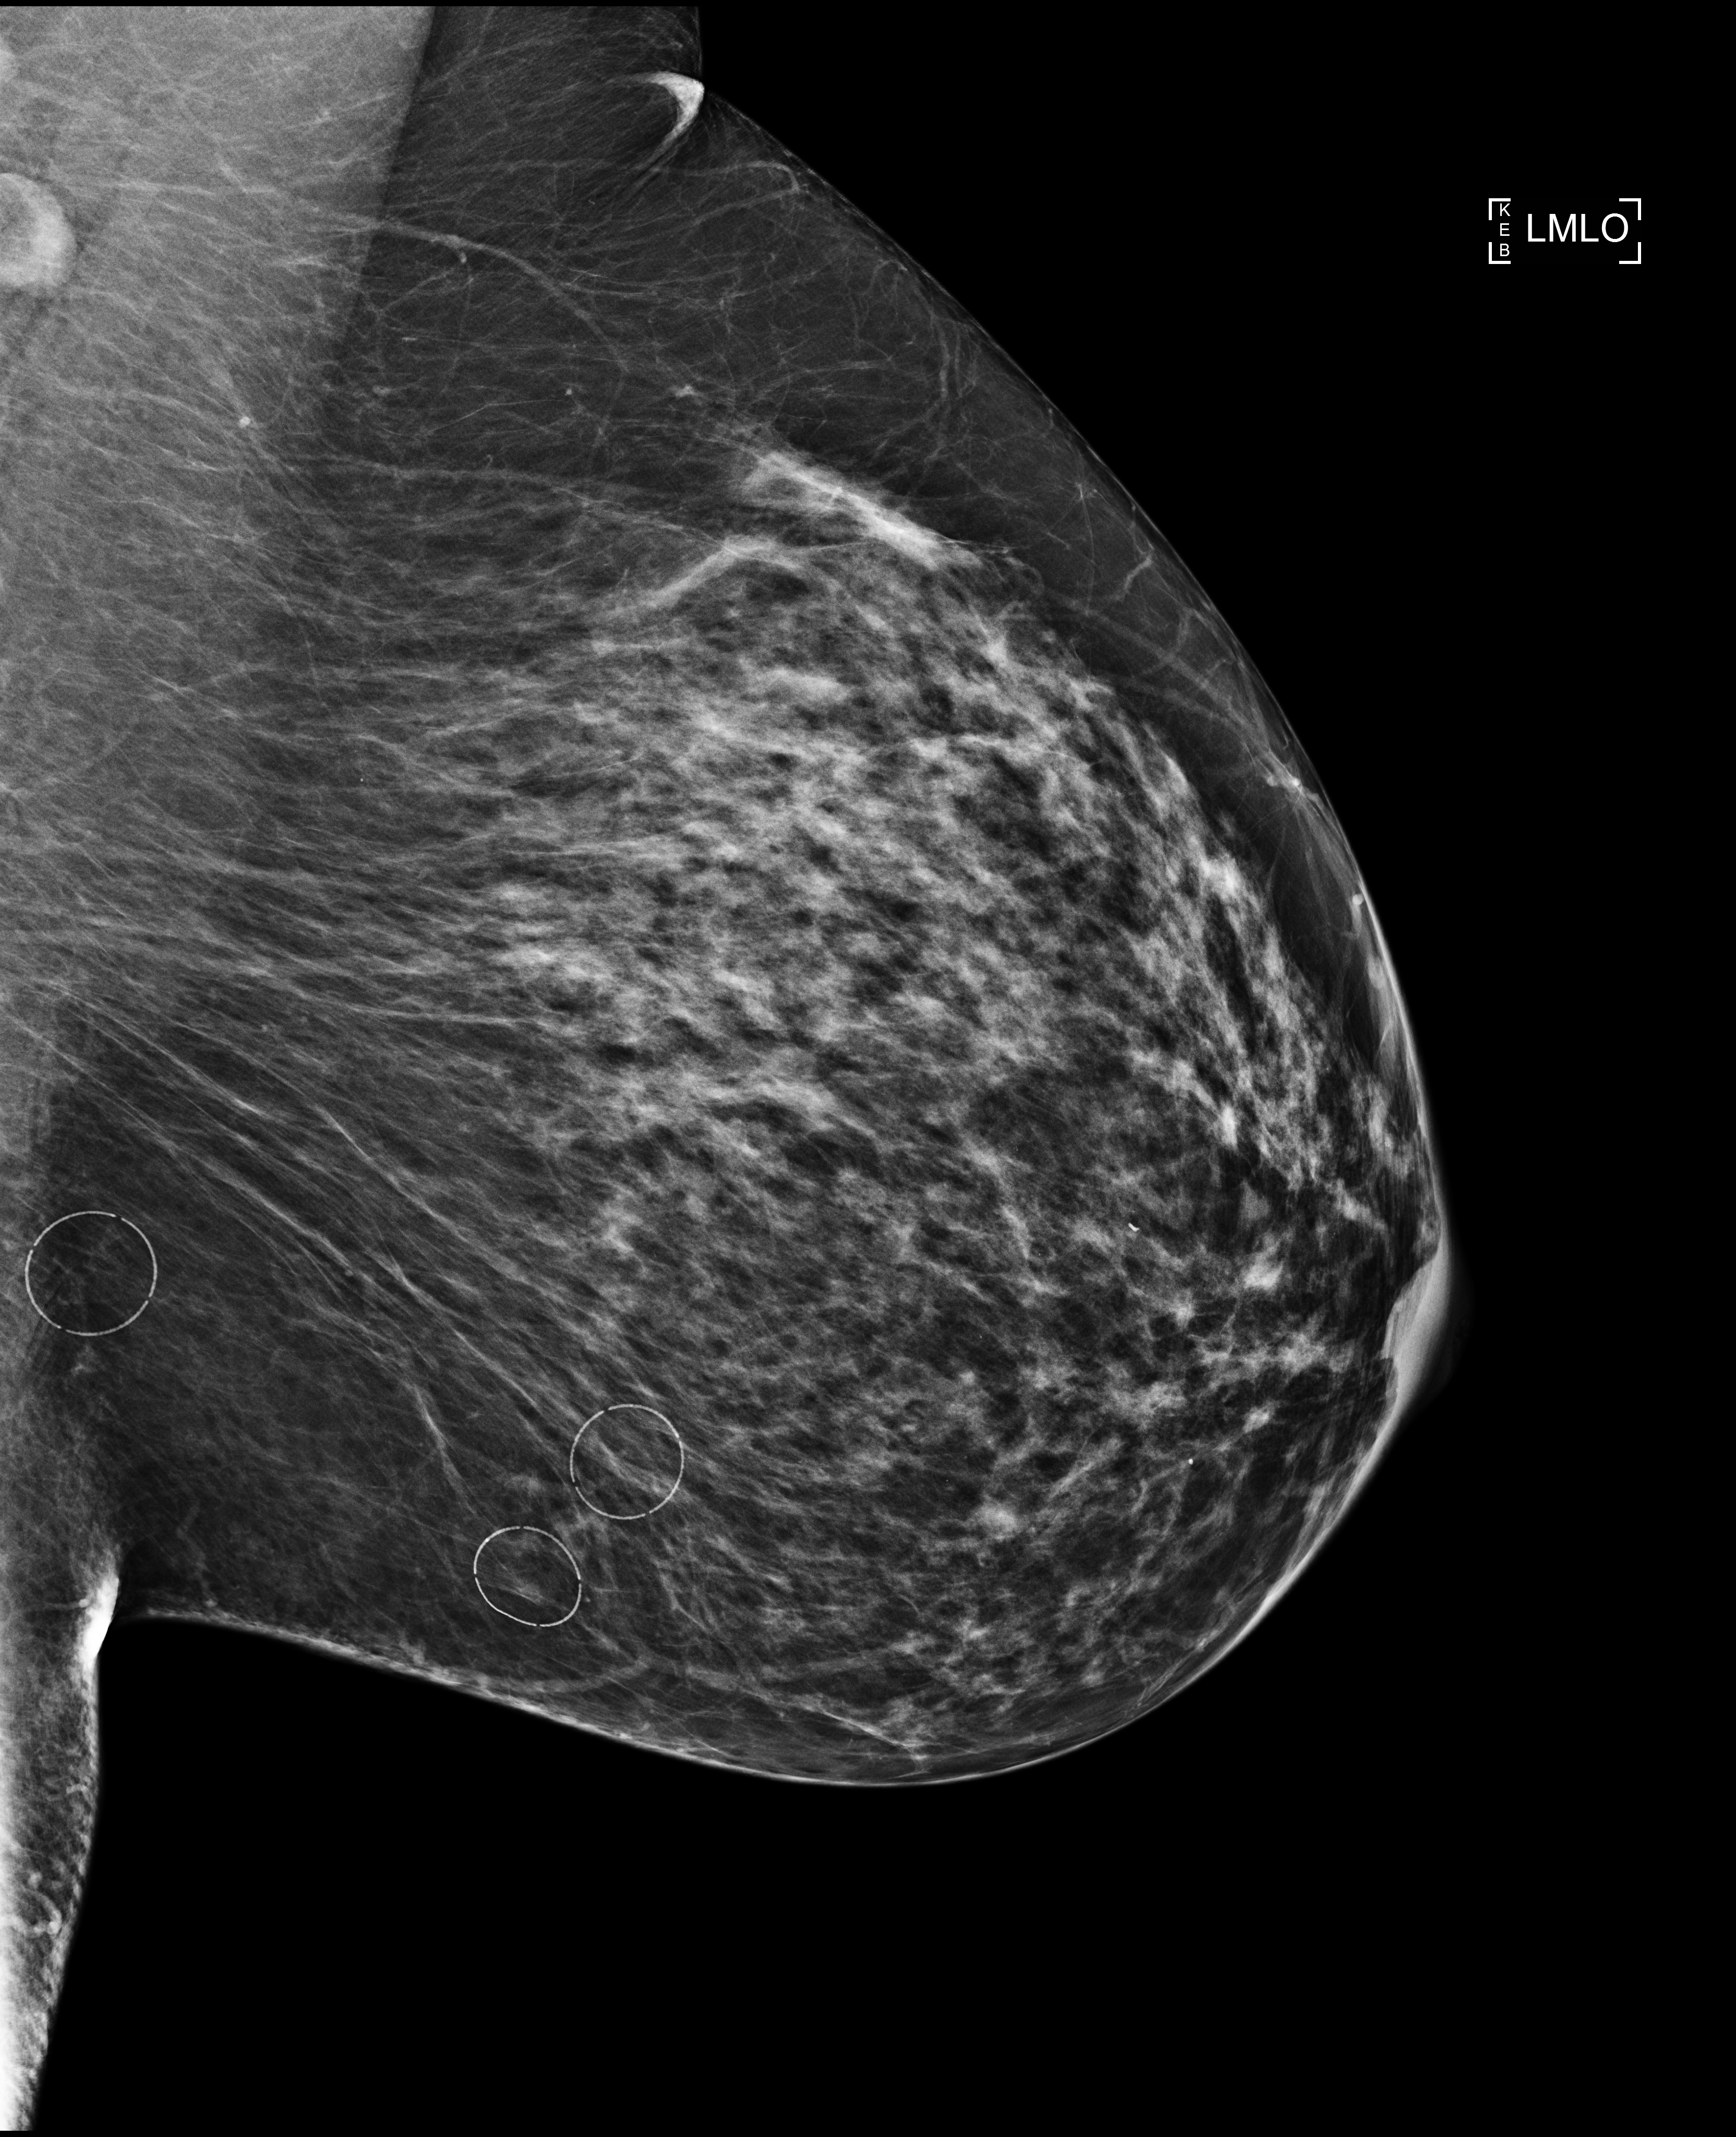
Screening examination; compressed breast thickness 72 mm. Patient aged 62 years (female).
Image type: full-field digital mammogram. Breast: left. Projection: mediolateral oblique (MLO) view.